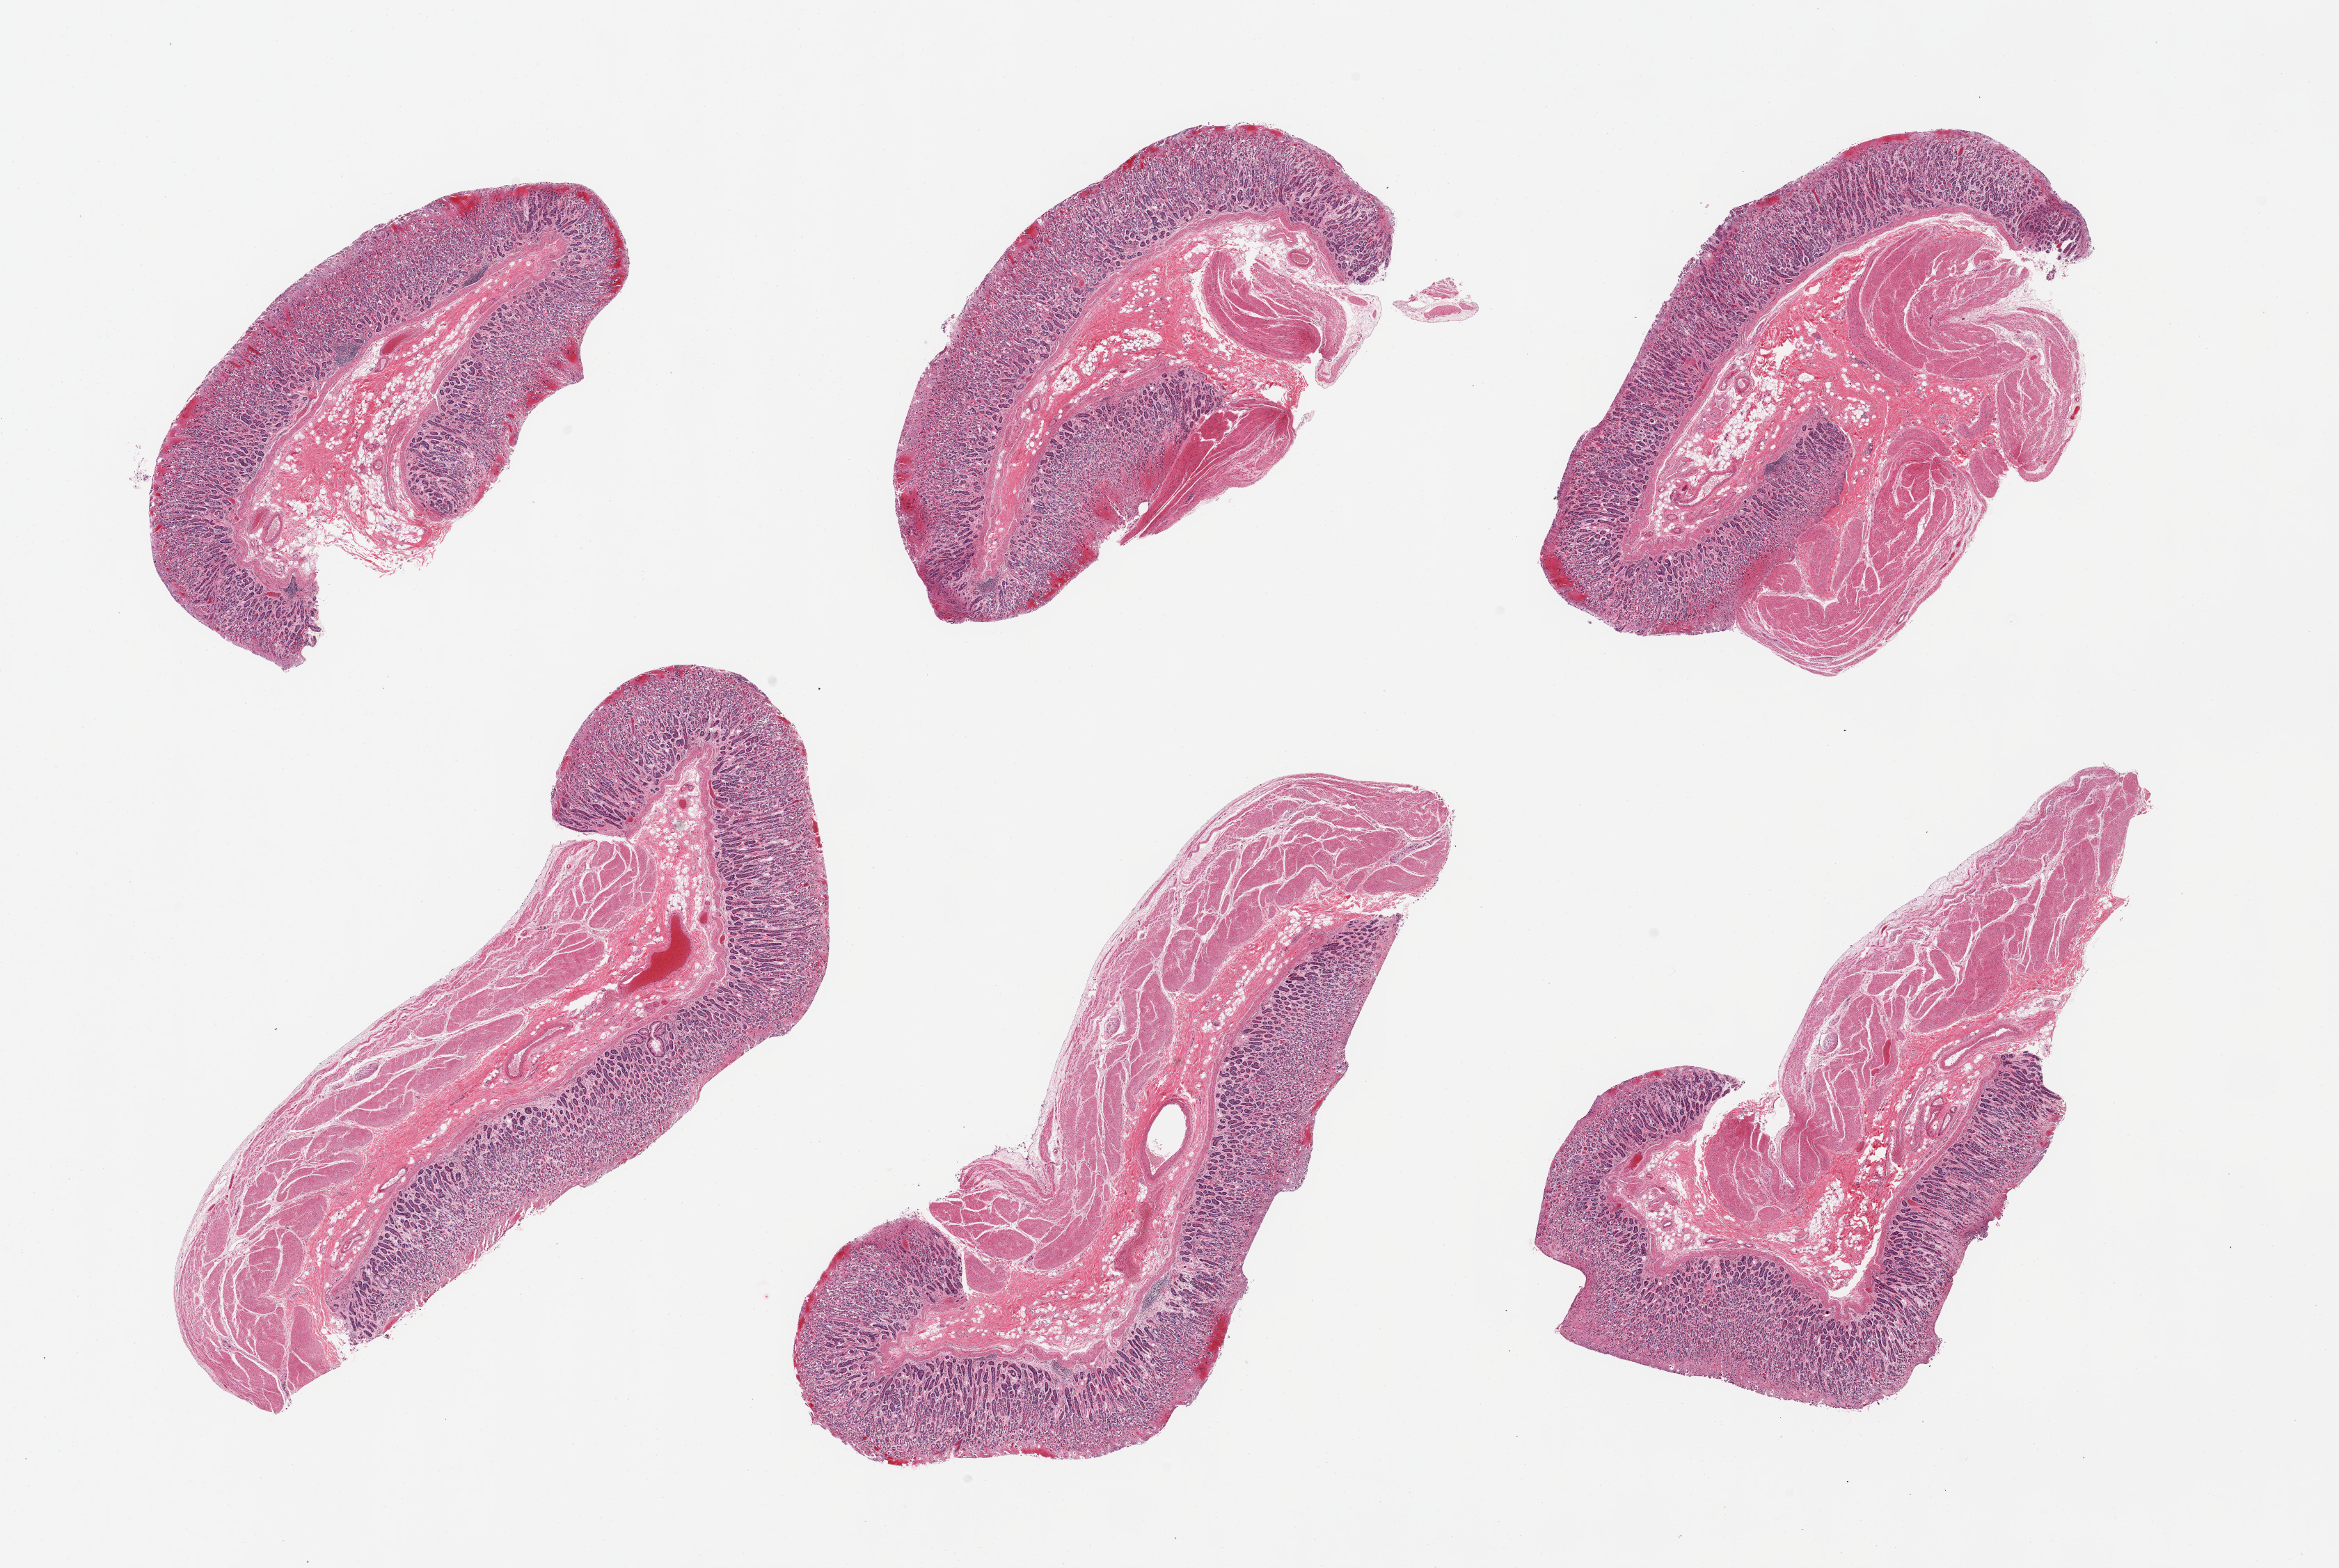
Hematoxylin and eosin (H&E) whole-slide image — low-resolution overview of the scanned area, about 26.6 x 17.8 mm (slide scanned at 20x), PAXgene-fixed, paraffin-embedded tissue, sampled site (target tissue): stomach, tissue donor sample.
Review note (as recorded): 6 pieces; 5 of 6 include mucosa and muscularis, last is mucosa only, autolysis of superficial (foveolar) glands.